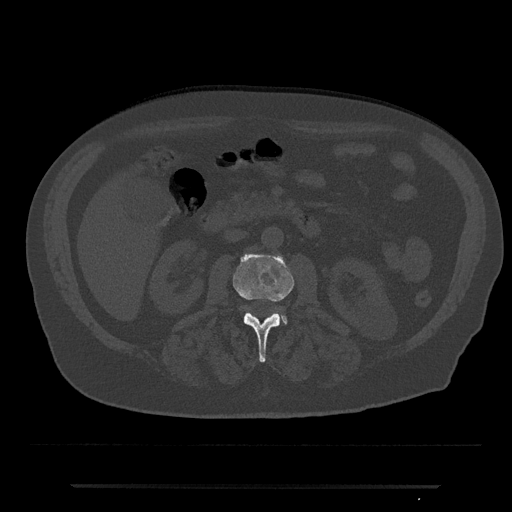
CT including the spine, one axial slice. Slice 456 of 797 in the series (ordered by position). Reconstruction kernel Br40s/3. Bone window (W 1800 / L 400 HU). 0.5 mm slice thickness. 512 × 512 image matrix. Patient: male, 80 years. From the clinical record (not read from this slice): primary cancer: prostate; vertebrae with lytic lesions (as recorded): L1, T11.
Annotated regions visible in this slice (semi-automatic segmentation, software-assisted and operator-edited):
- L2 vertebra: box from (x=232, y=254) to (x=294, y=363) px
- L3 vertebra: (x=281, y=314)–(x=288, y=324)